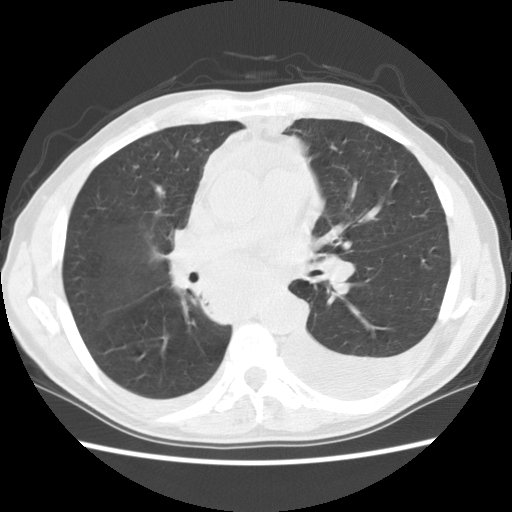
Low-dose screening chest CT, axial slice, first (baseline) screen, lung window (W 1500 / L -600 HU), 2.5 mm slice thickness, standard (soft-tissue) reconstruction kernel (STANDARD), 512 × 512 image matrix, field of view 346 × 346 mm. Male participant, aged 60 years at enrolment.
Expert-annotated lung lesion, bounding box <175,239,301,330> (left, top, right, bottom; pixels). Screening reader's record for this exam: no non-calcified nodule ≥4 mm recorded. Official screen result: negative screen, significant abnormalities not suspicious for lung cancer. Later outcome: lung cancer diagnosed 12 days after this screen — squamous cell carcinoma, NOS, carina, poorly differentiated (G3), stage IV (AJCC 6th edition).